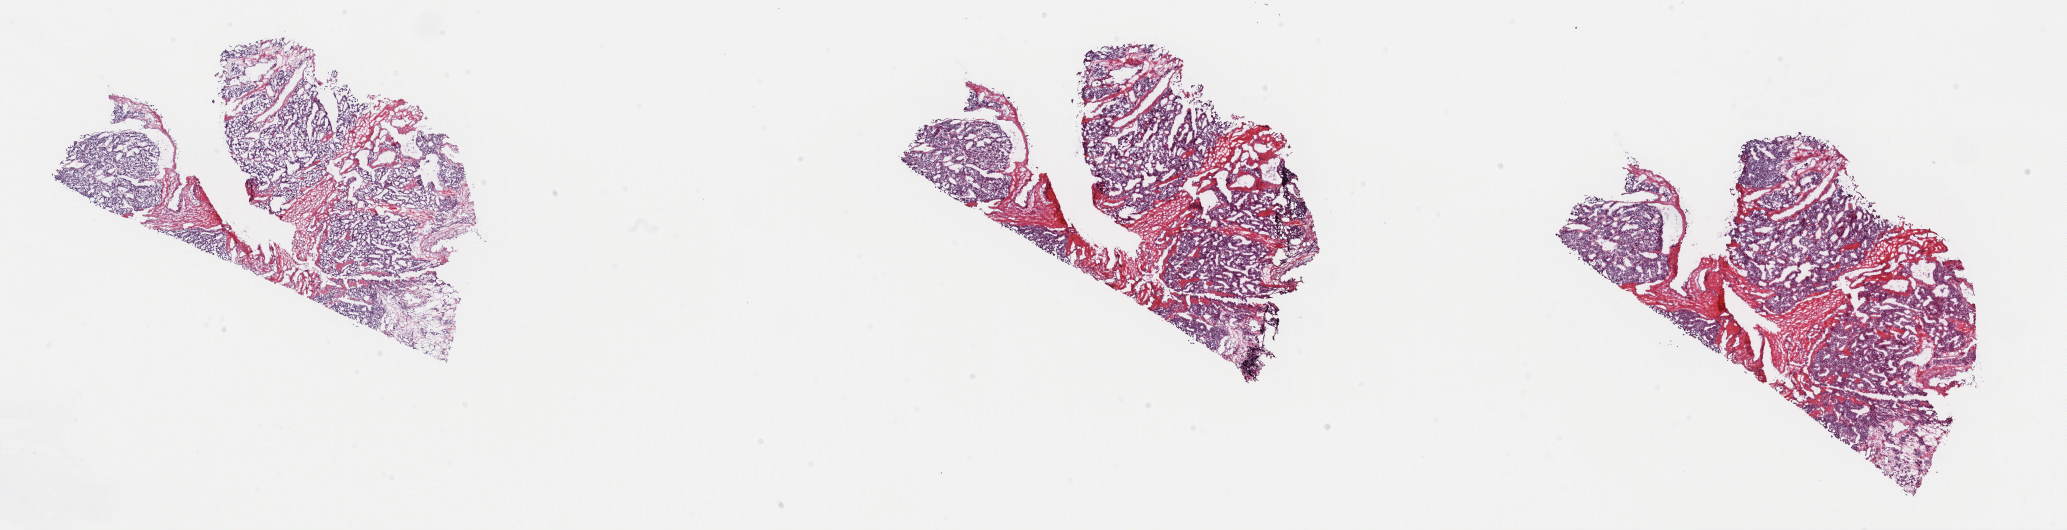
Whole-slide histology image, H&E, a low-resolution overview of the entire scanned area, about 32.7 x 8.4 mm (from a 40x scan); frozen section from the top of the tissue portion; primary tumour sample. Female, age 41 years at initial diagnosis. Slide review estimates, as recorded: tumour cells 60%, tumour nuclei 60%, normal cells 0%, stromal cells 20%, necrosis 20%. Infiltration values recorded for this section: lymphocyte infiltration 40%, monocyte infiltration 20%, neutrophil infiltration 20%.
Pathologic diagnosis: Extra-adrenal paraganglioma, malignant. Laterality: left.